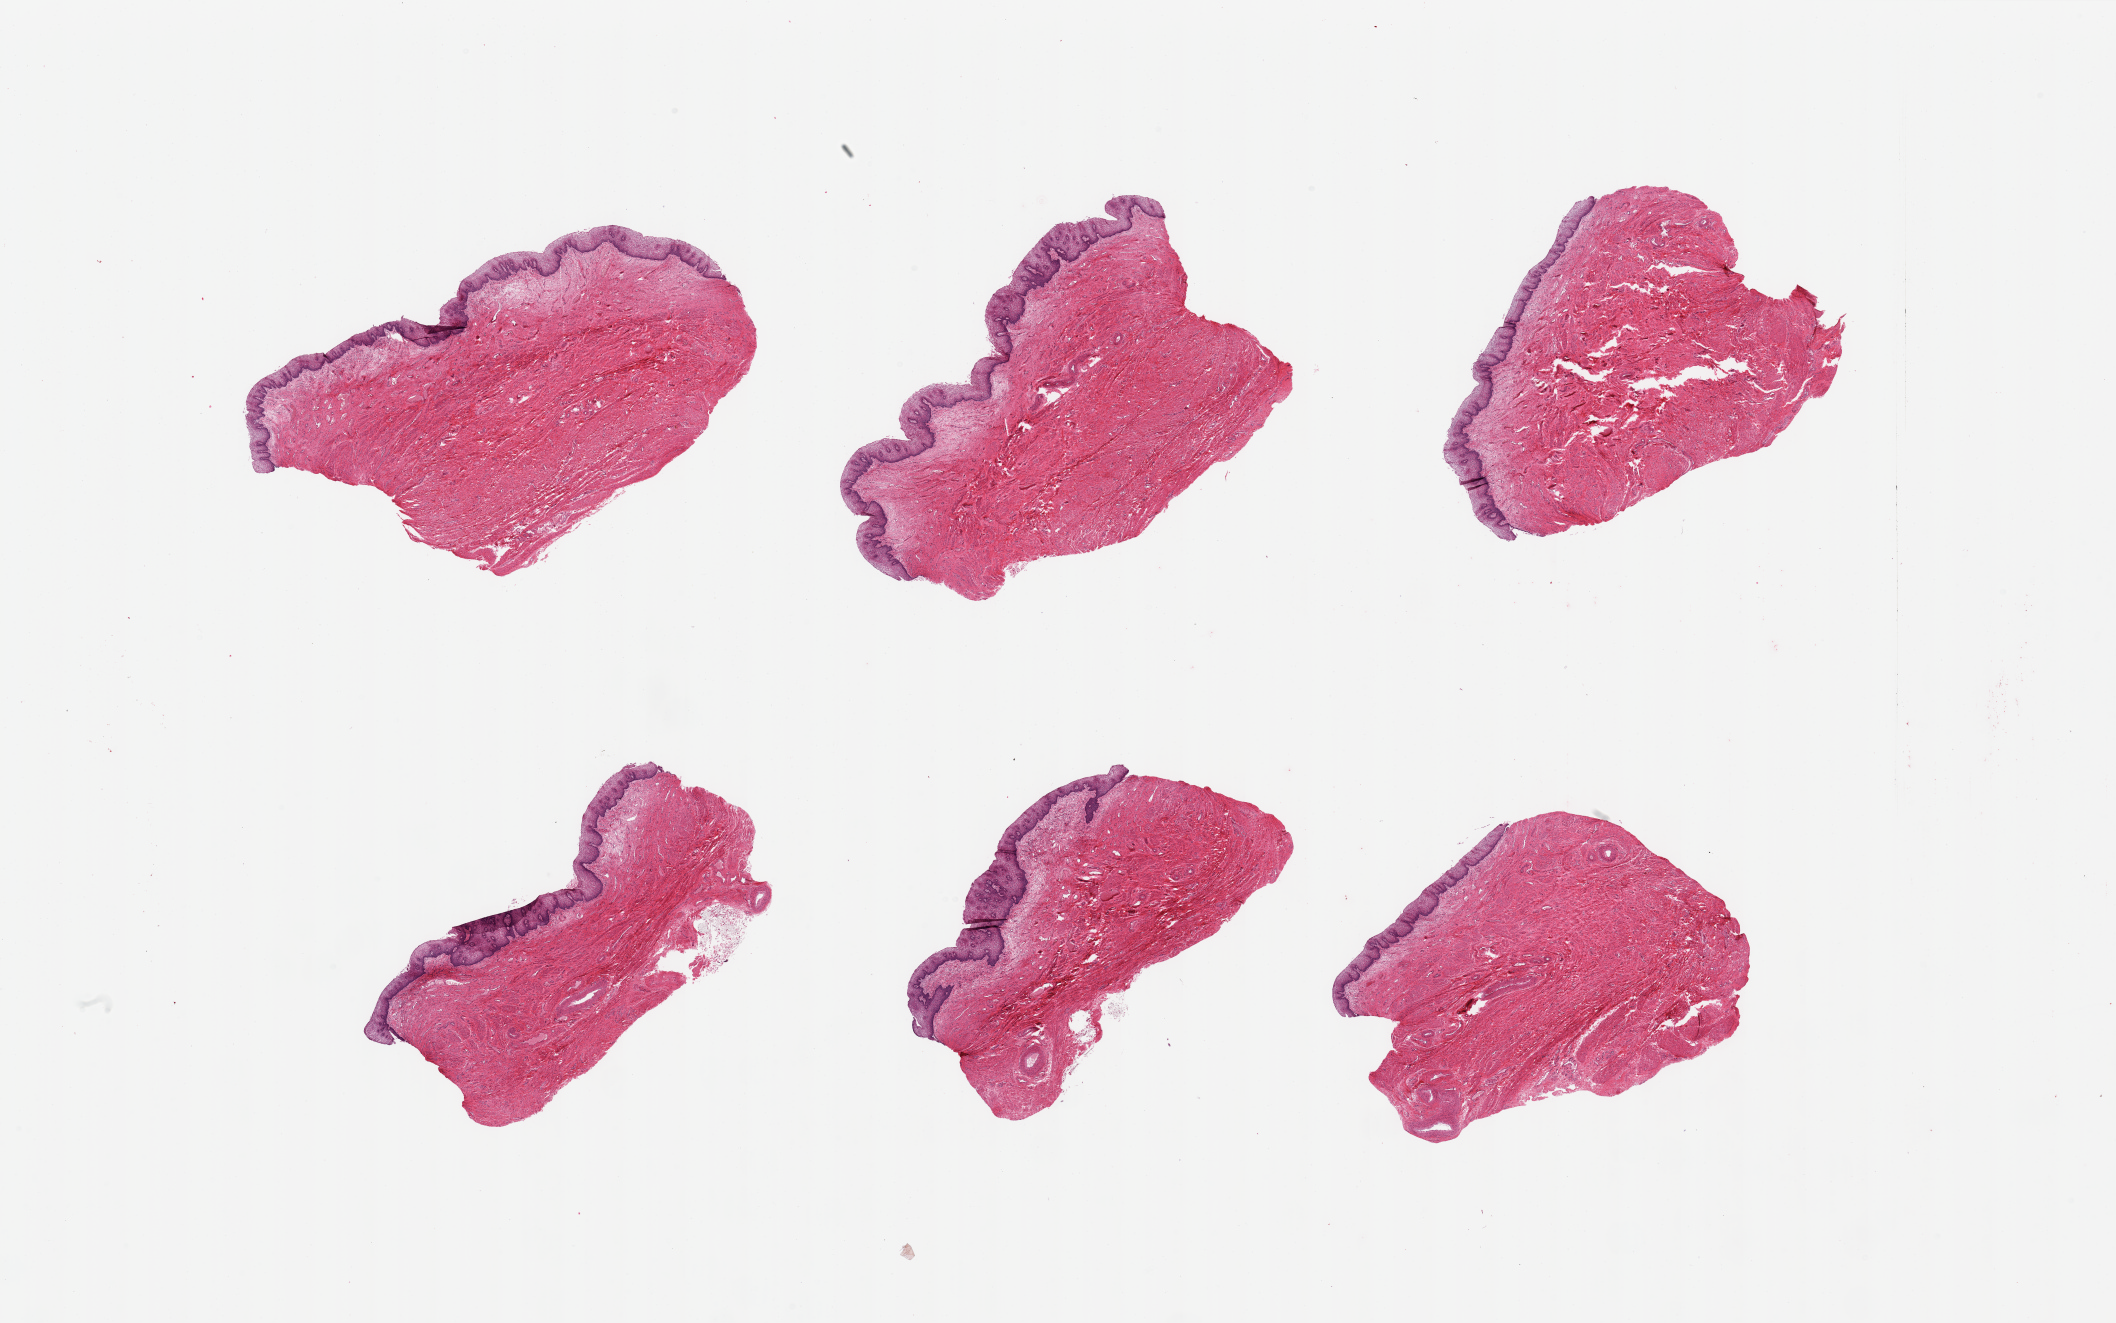
Hematoxylin and eosin (H&E) whole-slide image — shown as a low-resolution overview of the whole scanned area (about 33.5 x 20.9 mm). PAXgene-fixed paraffin-embedded (PFPE) section. Section of vagina (target tissue). Donor tissue sample. Female donor.
Pathologist's review note for this sample: 6 pieces; all have epithelium.